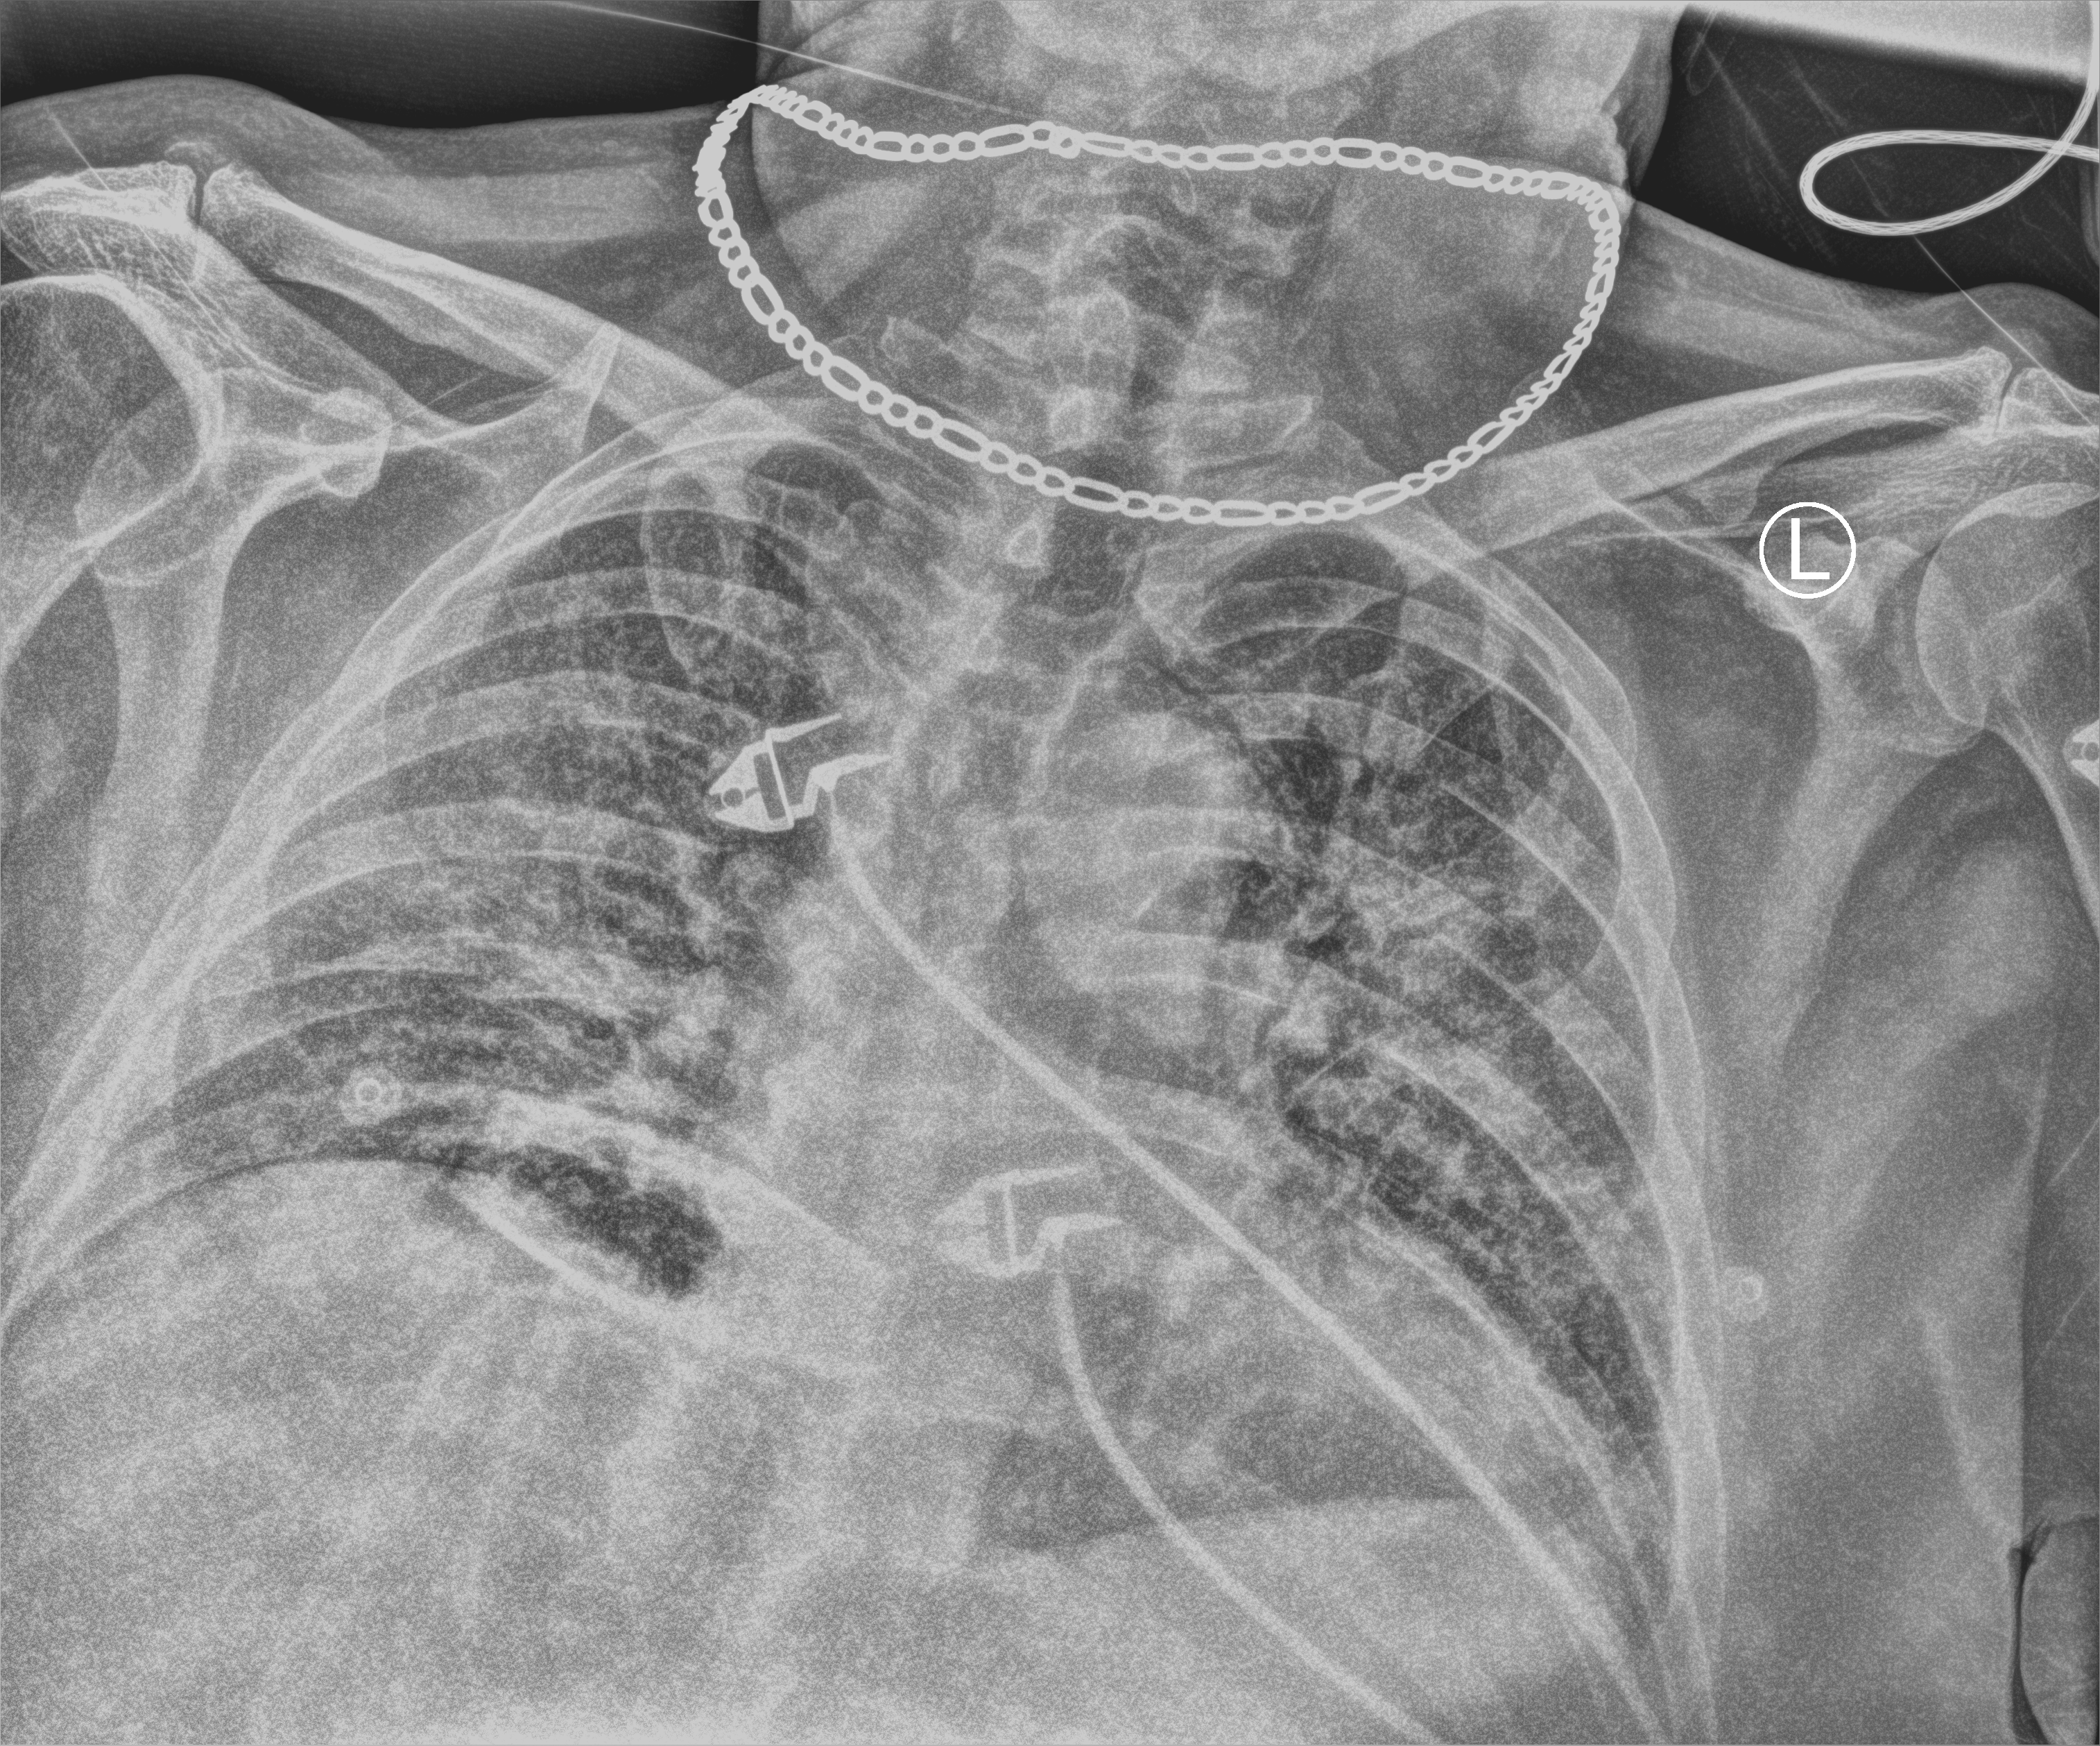
Chest X-ray (portable); anteroposterior (AP) projection. Patient hospitalised with COVID-19; male, aged 60–74 years.
From the hospital-stay record, not from the radiograph (when in the stay this image was taken is not recorded): admitted to intensive care during this hospital stay: no; mechanically ventilated during this hospital stay: no.